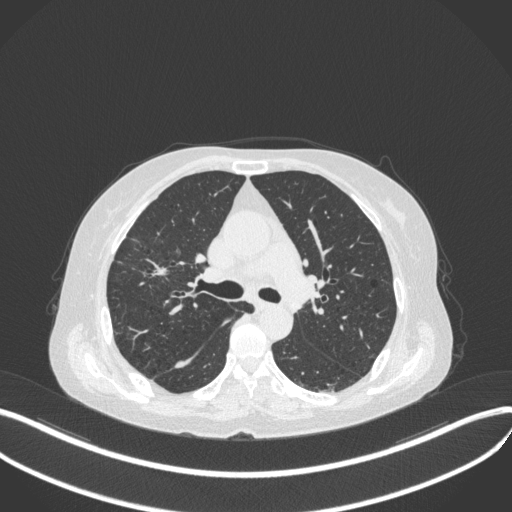
Chest CT, one axial slice; reconstruction kernel B31f; 120 kVp; lung window (W 1500 / L -600 HU); 1 mm slice thickness; 512 × 512 image matrix, field of view 400 × 400 mm. Female patient, age 69 years. From the clinical record (not read from this slice): clinical TNM (as recorded): T1b N3 M0.
Annotated regions visible in this slice (rectangle marked by the reading radiologist):
- lung tumour (recorded histology: small cell carcinoma): bounding box [x1, y1, x2, y2] px = [139, 252, 177, 282]